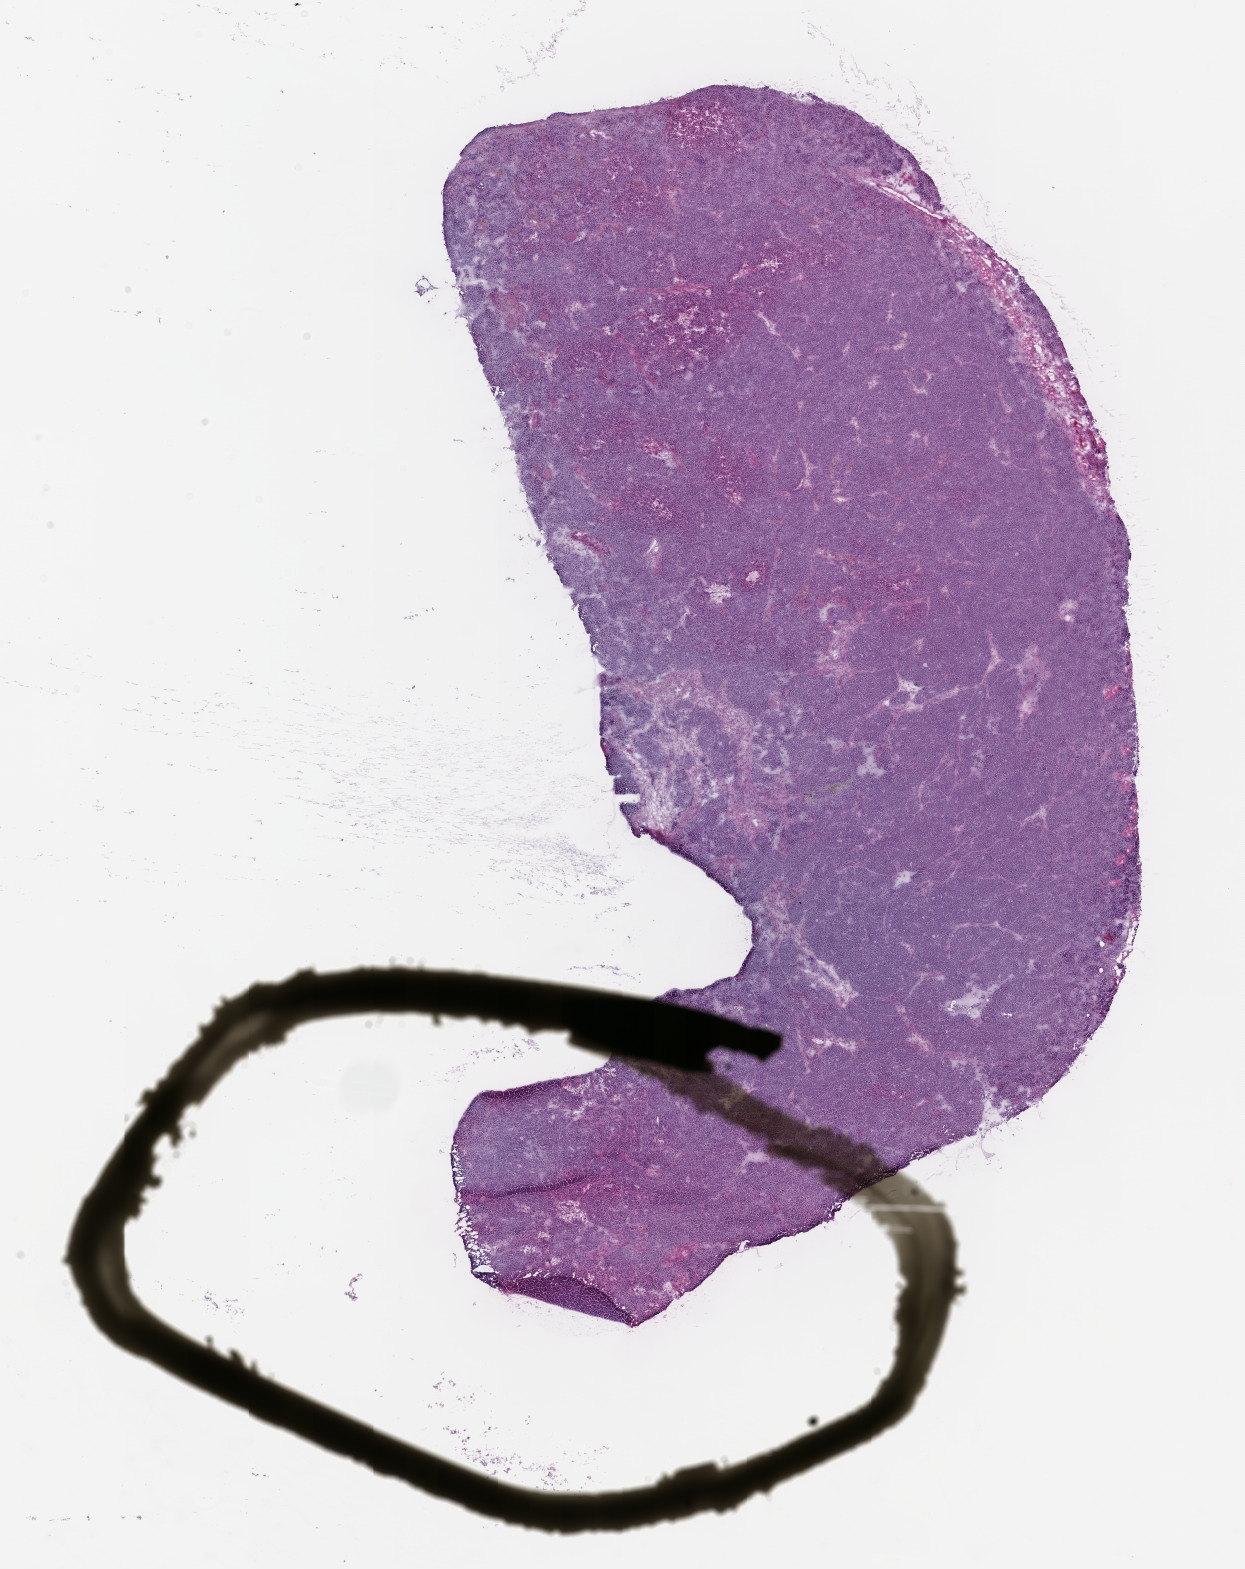
H&E whole-slide image of a patient-derived xenograft (PDX) tumor grown in a mouse, shown as a low-resolution overview of the whole scanned area (about 10.0 x 12.6 mm). Formalin-fixed paraffin-embedded section. Tumor site category: prostate.
Originating patient diagnosis: Prostate Carcinoma.